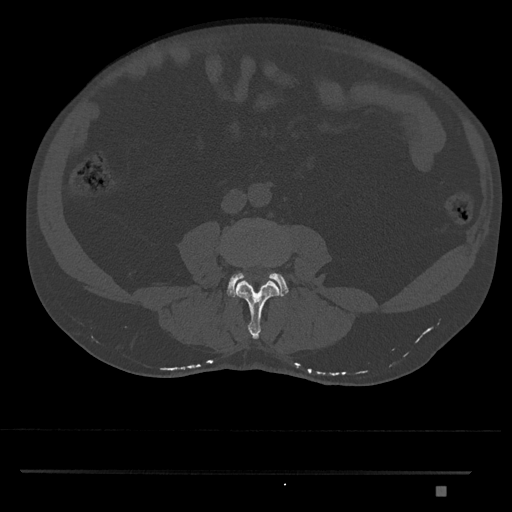
CT including the spine, one axial slice. Position 655 of 1134 along the scan axis. Reconstruction kernel Br40s/3. 120 kVp. Bone window (W 1800 / L 400 HU). 0.5 mm slice thickness. 512 × 512 image matrix, field of view 429 × 429 mm. Male patient, age 65 years. From the clinical record (not read from this slice): primary cancer: prostate.
Structures marked on this image (semi-automatically segmented with operator editing):
- L3 vertebra: bounding box (x1, y1, x2, y2) in pixels: (235, 281, 280, 339)
- L4 vertebra: (227, 272, 289, 298)